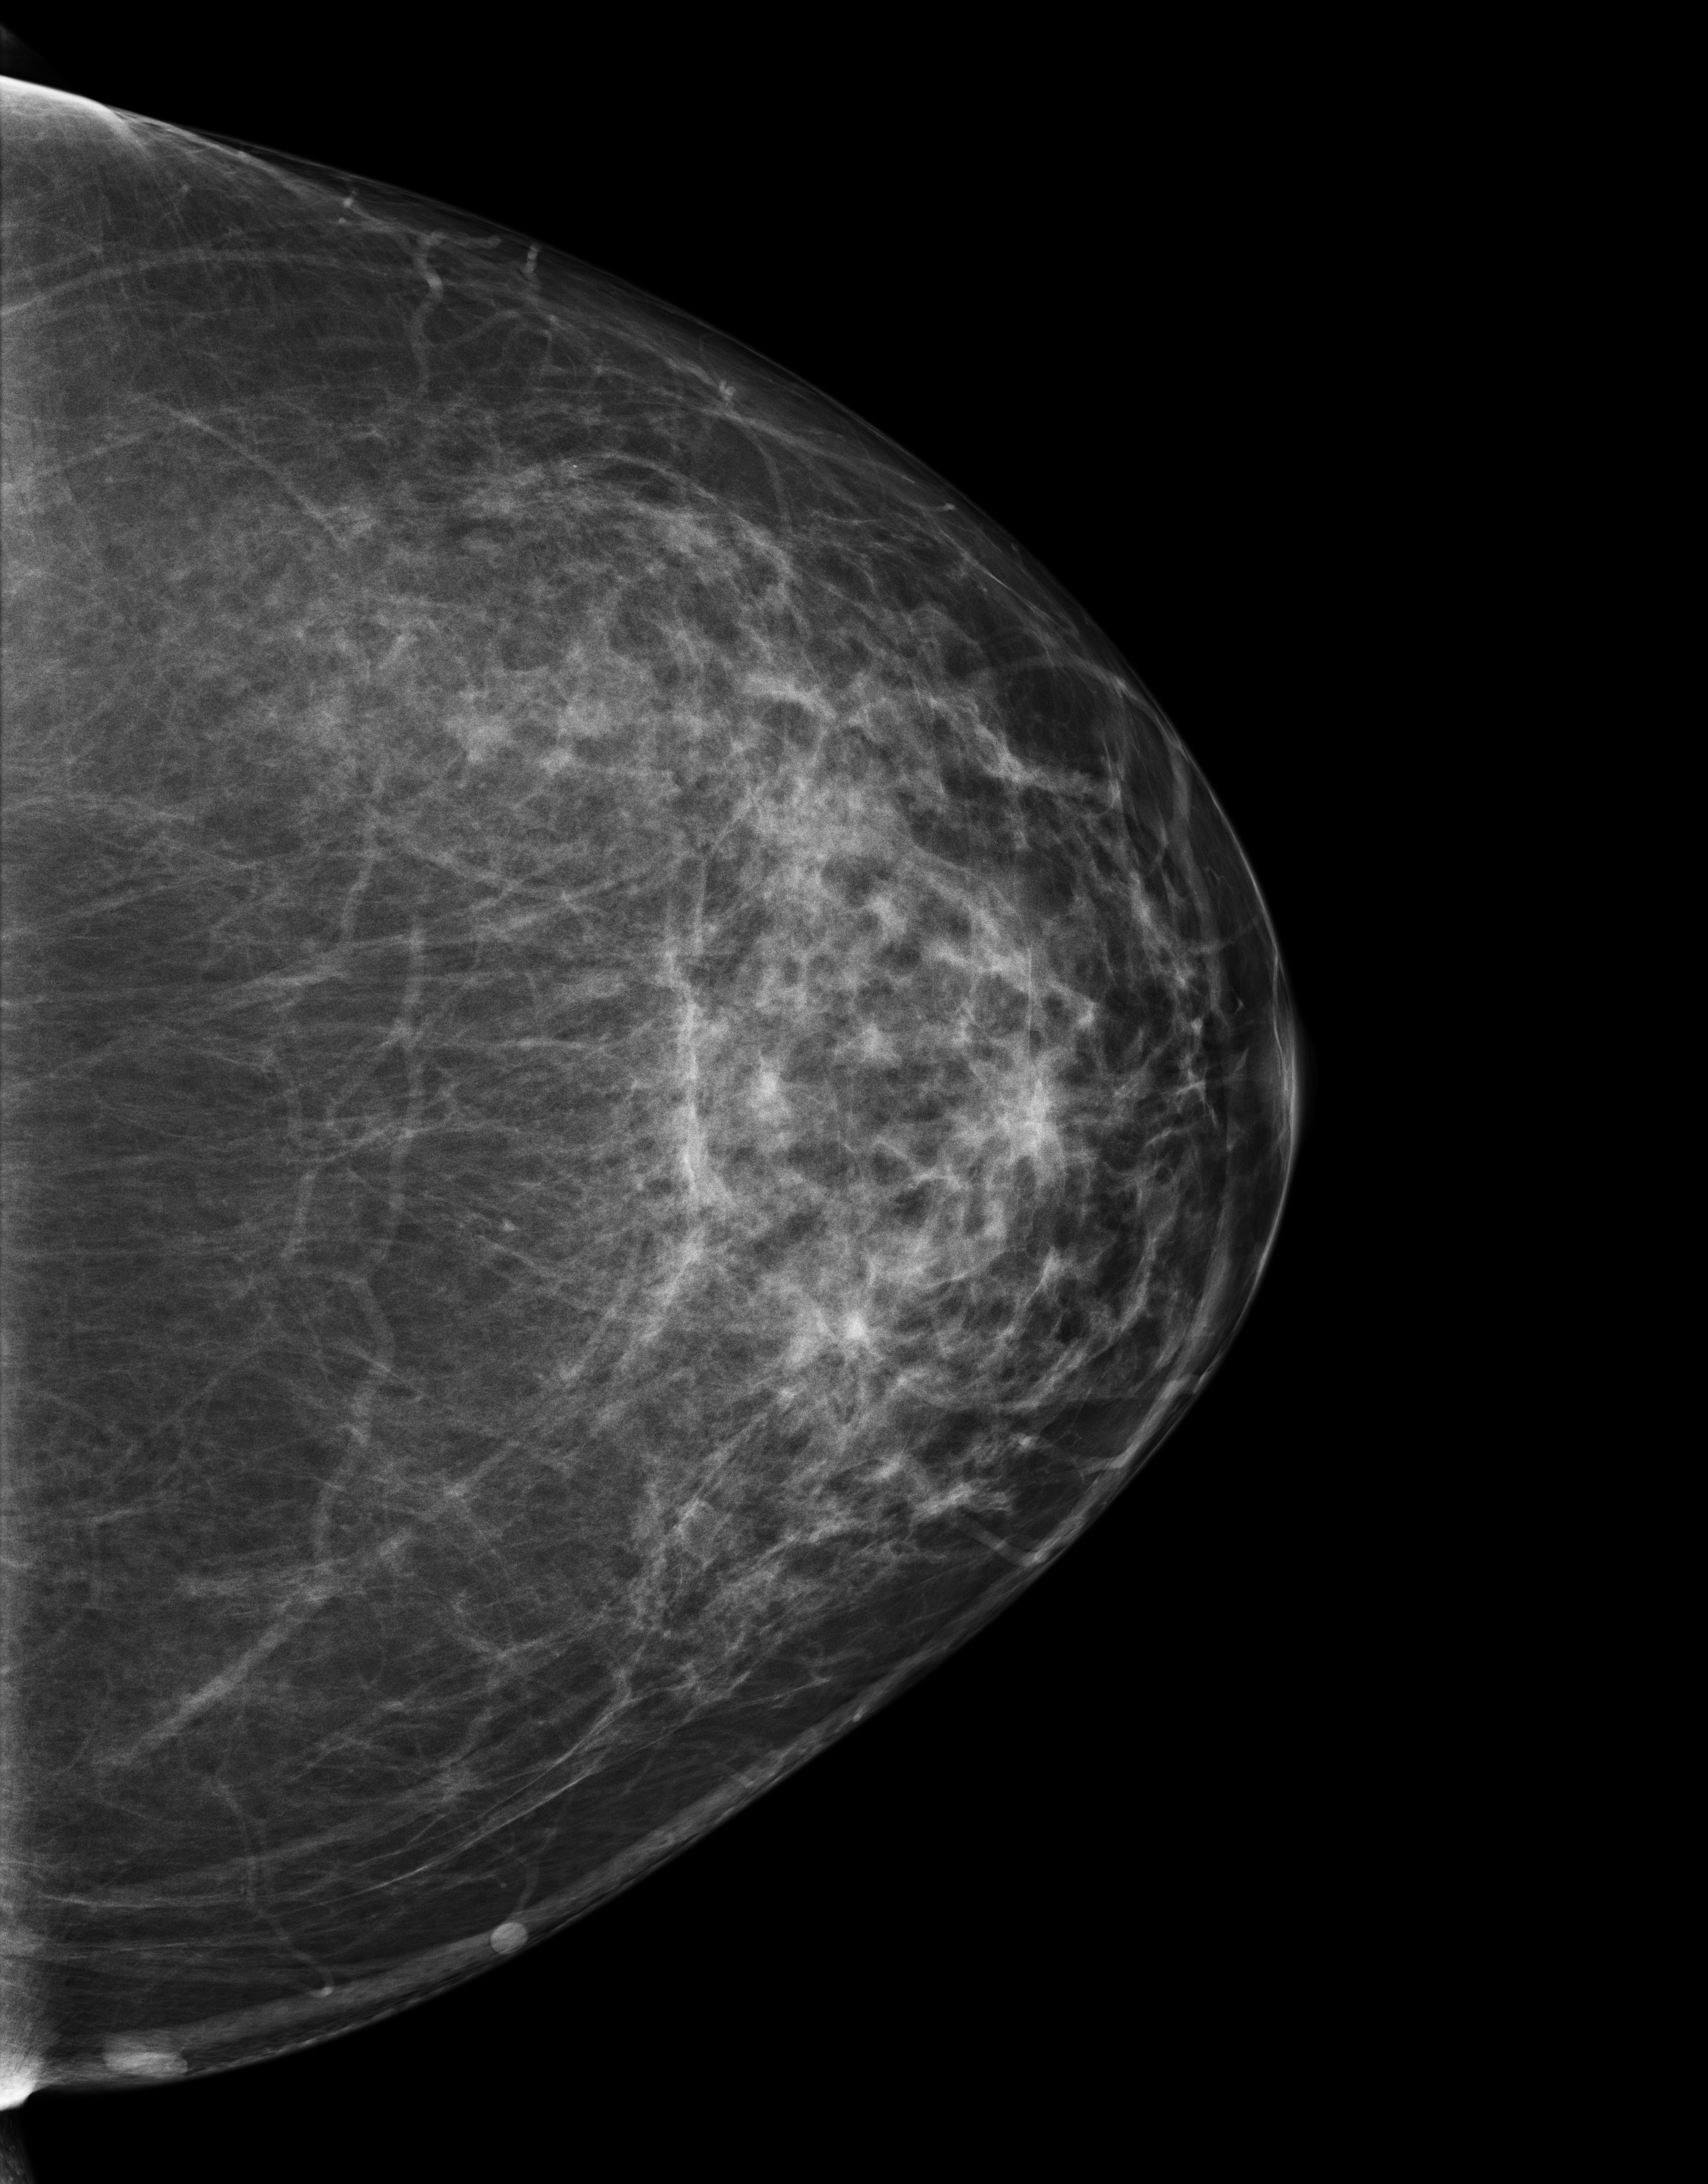
Screening examination; compressed breast thickness 81 mm; system: Senographe Essential ADS_56.21.3. Patient: female, 58 years.
Image type: full-field digital mammogram. Breast: left. Projection: CC view.